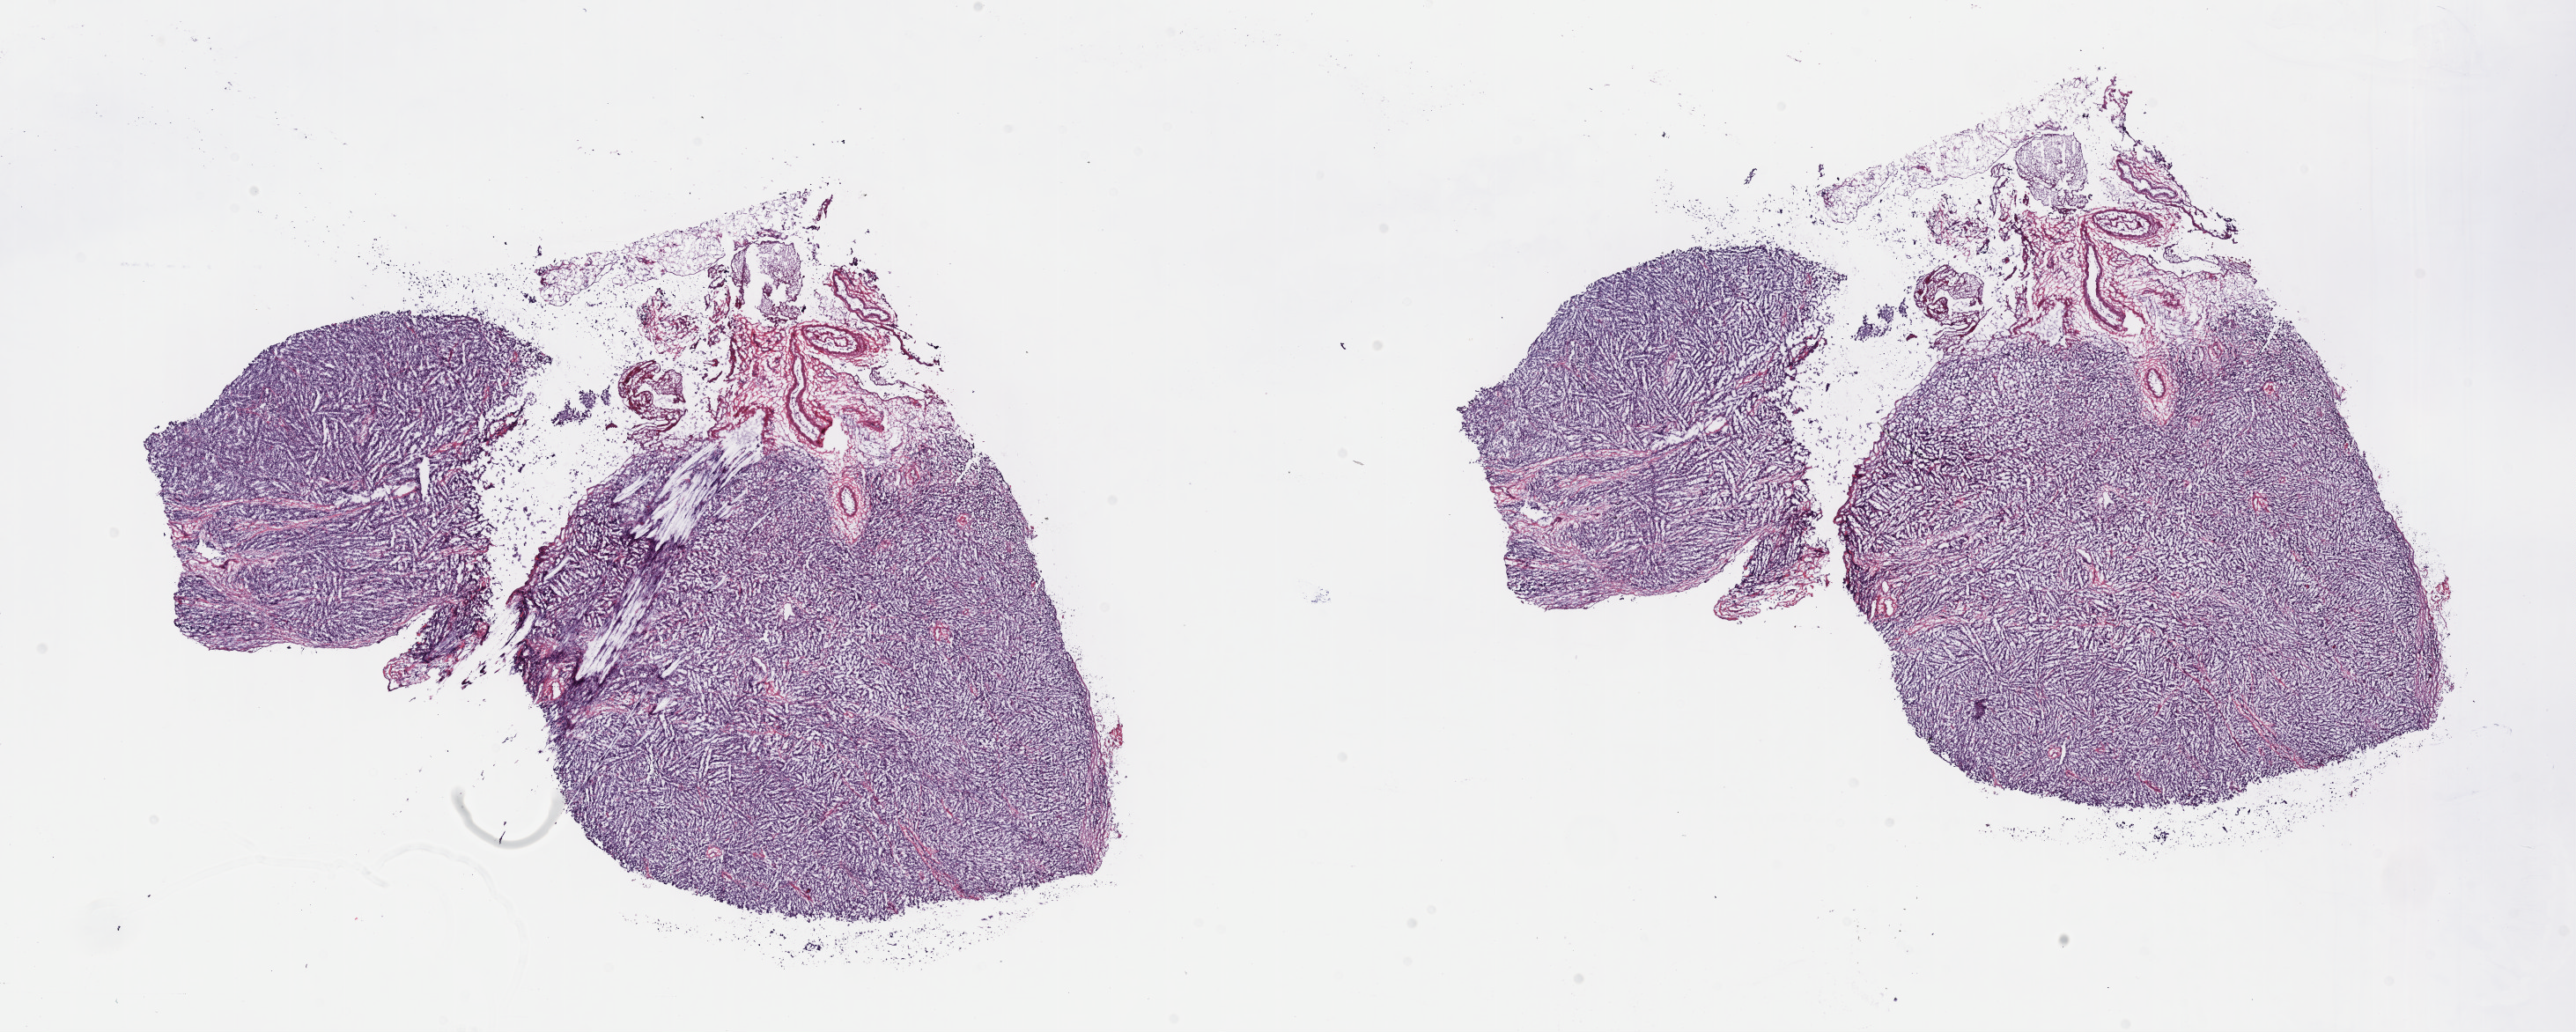
Digitized H&E tissue section (whole slide) — shown as a low-resolution overview of the whole scanned area (about 23.7 x 9.5 mm, acquisition: 40x scan), frozen section from the top of the tissue portion, thymus, primary tumour sample. Male, age 63 years at initial diagnosis. Slide review estimates, as recorded: tumour cells 70%, tumour nuclei 85%, normal cells 30%, stromal cells 0%, necrosis 0%. Infiltration values recorded for this section: lymphocyte infiltration 0%, monocyte infiltration 0%, neutrophil infiltration 0%.
- histologic diagnosis: Thymic carcinoma, NOS